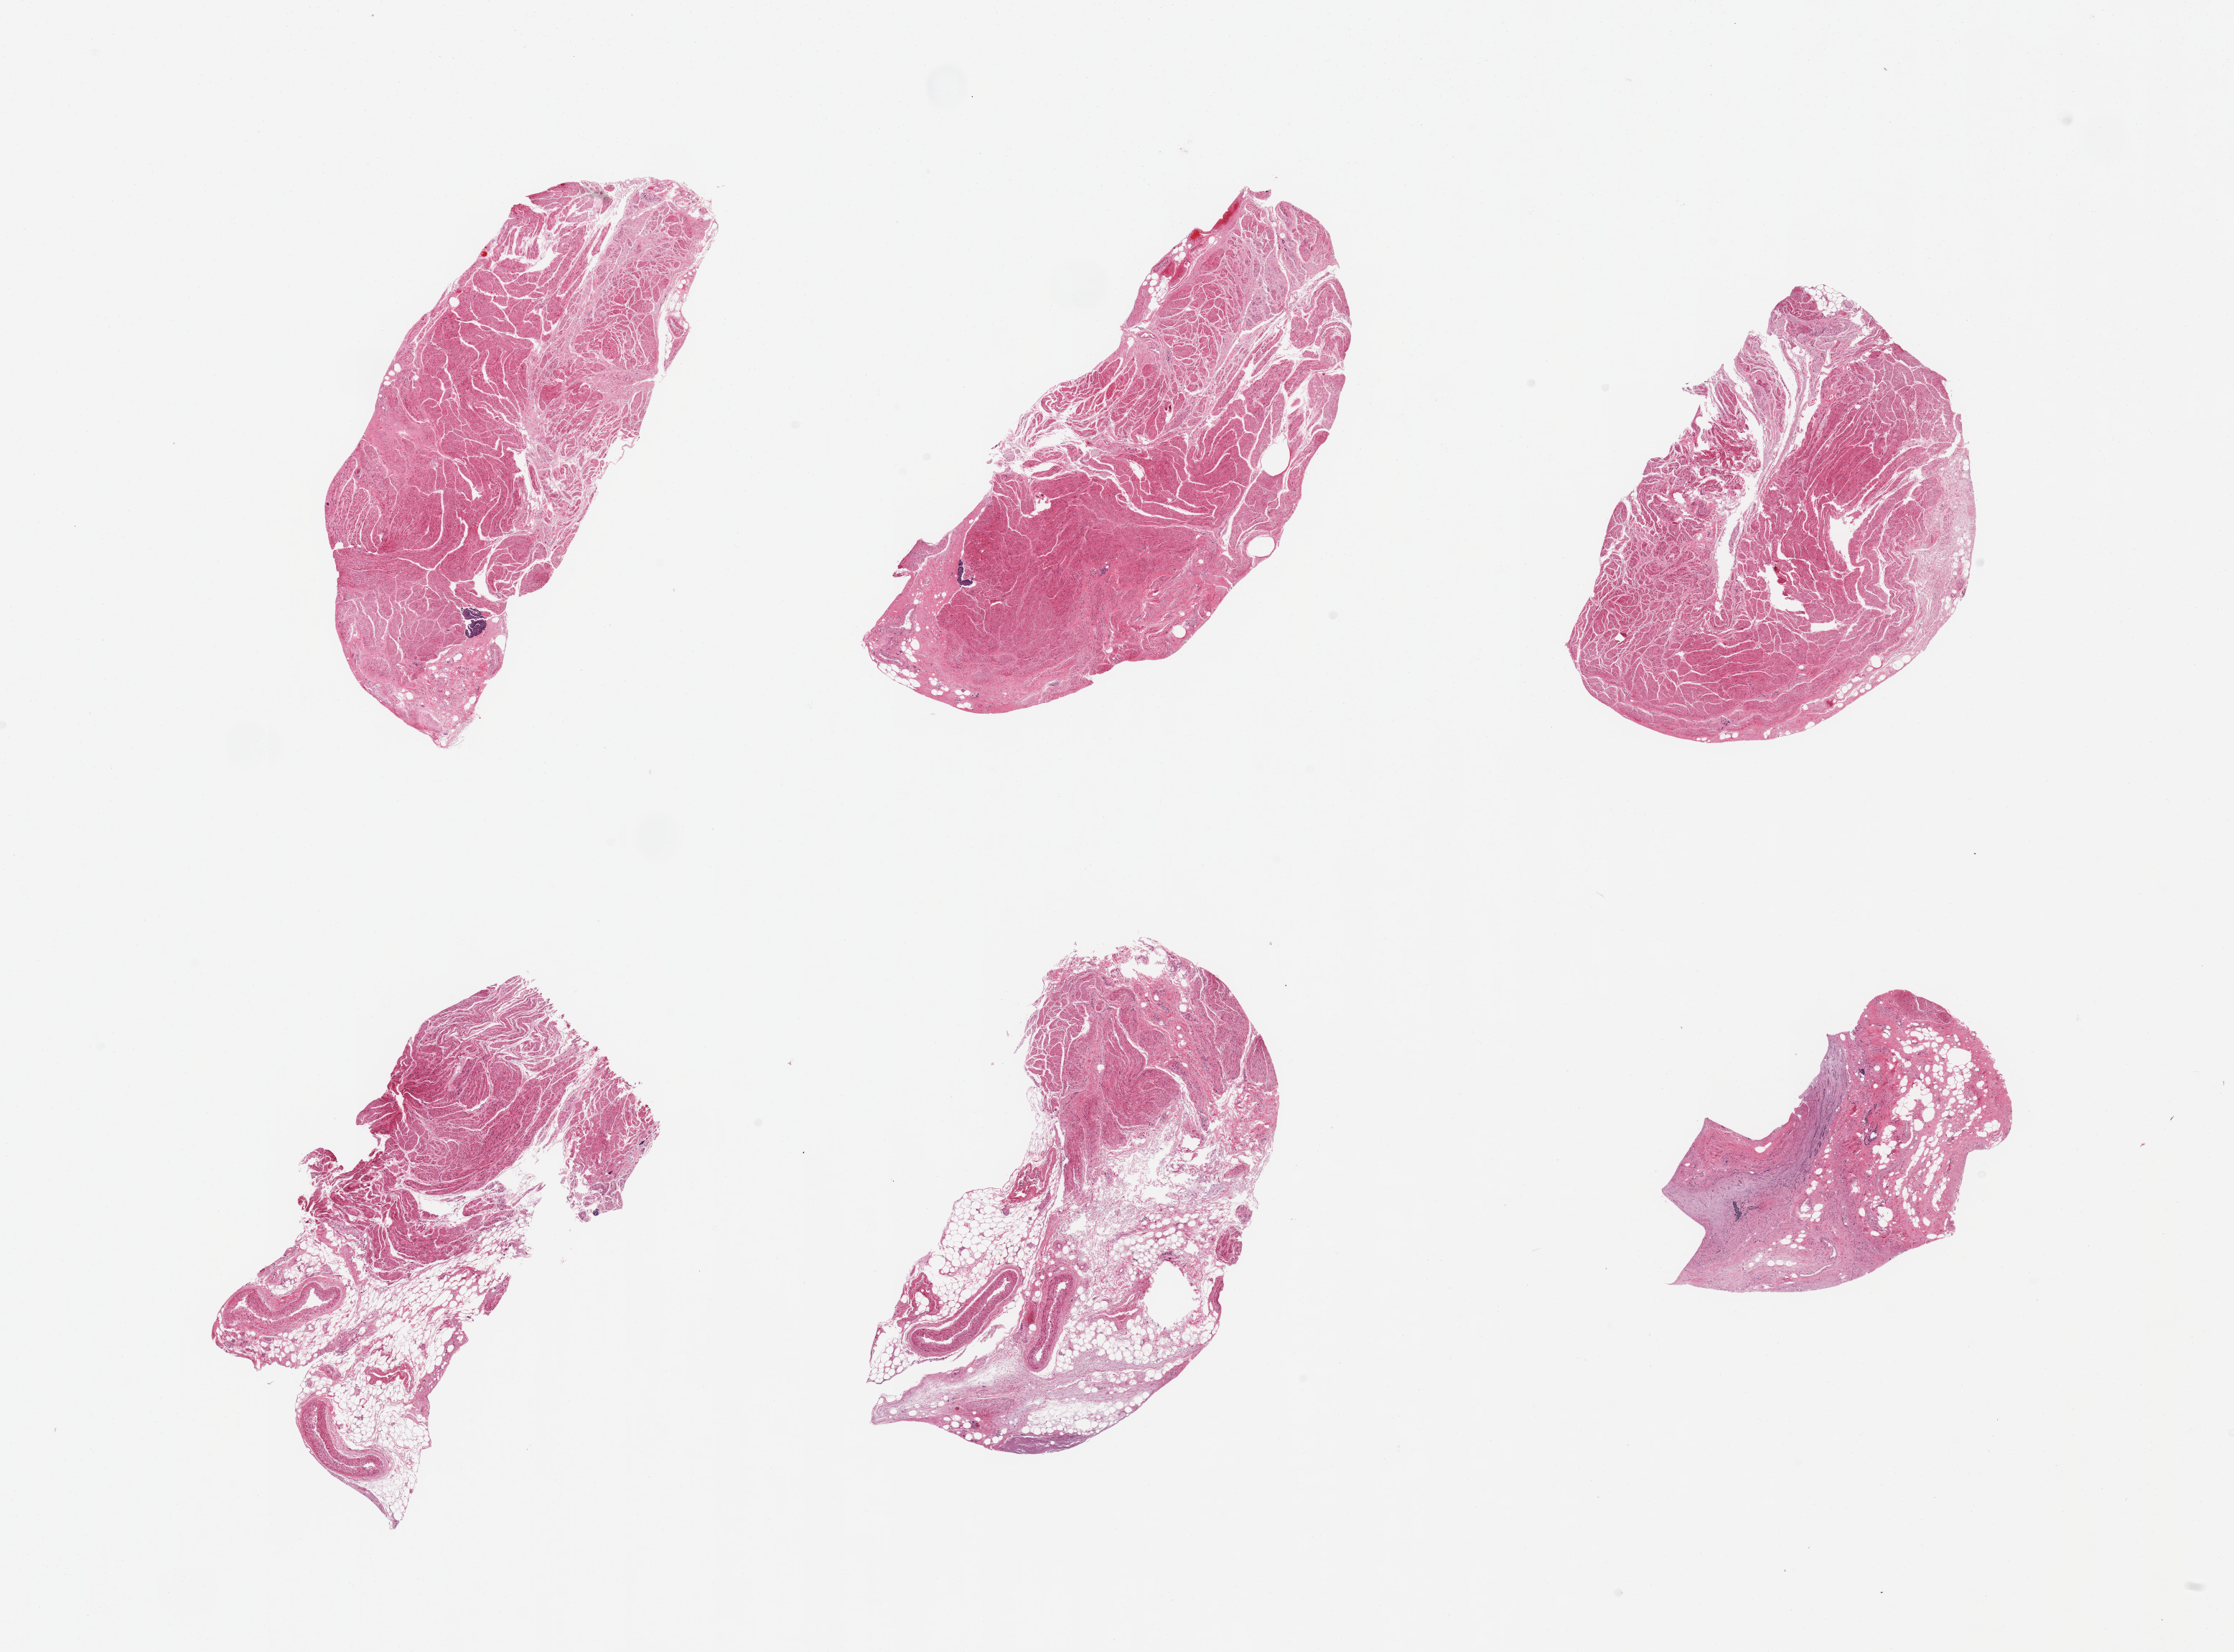
Whole-slide image, hematoxylin and eosin (H&E) stain, shown as a low-resolution overview of the whole scanned area (about 24.6 x 18.2 mm, slide scanned at 20x), PAXgene-fixed paraffin-embedded (PFPE) section, target tissue: gastroesophageal junction, tissue donor sample. Donor sex: male.
• reviewer comment on this tissue sample: 6 pieces; 3 have all muscularis (1 with 0.3mm squamous carry-over-labeled), 2 have 30% muscle, remainder fat and stroma; 1 has no muscle, all stroma